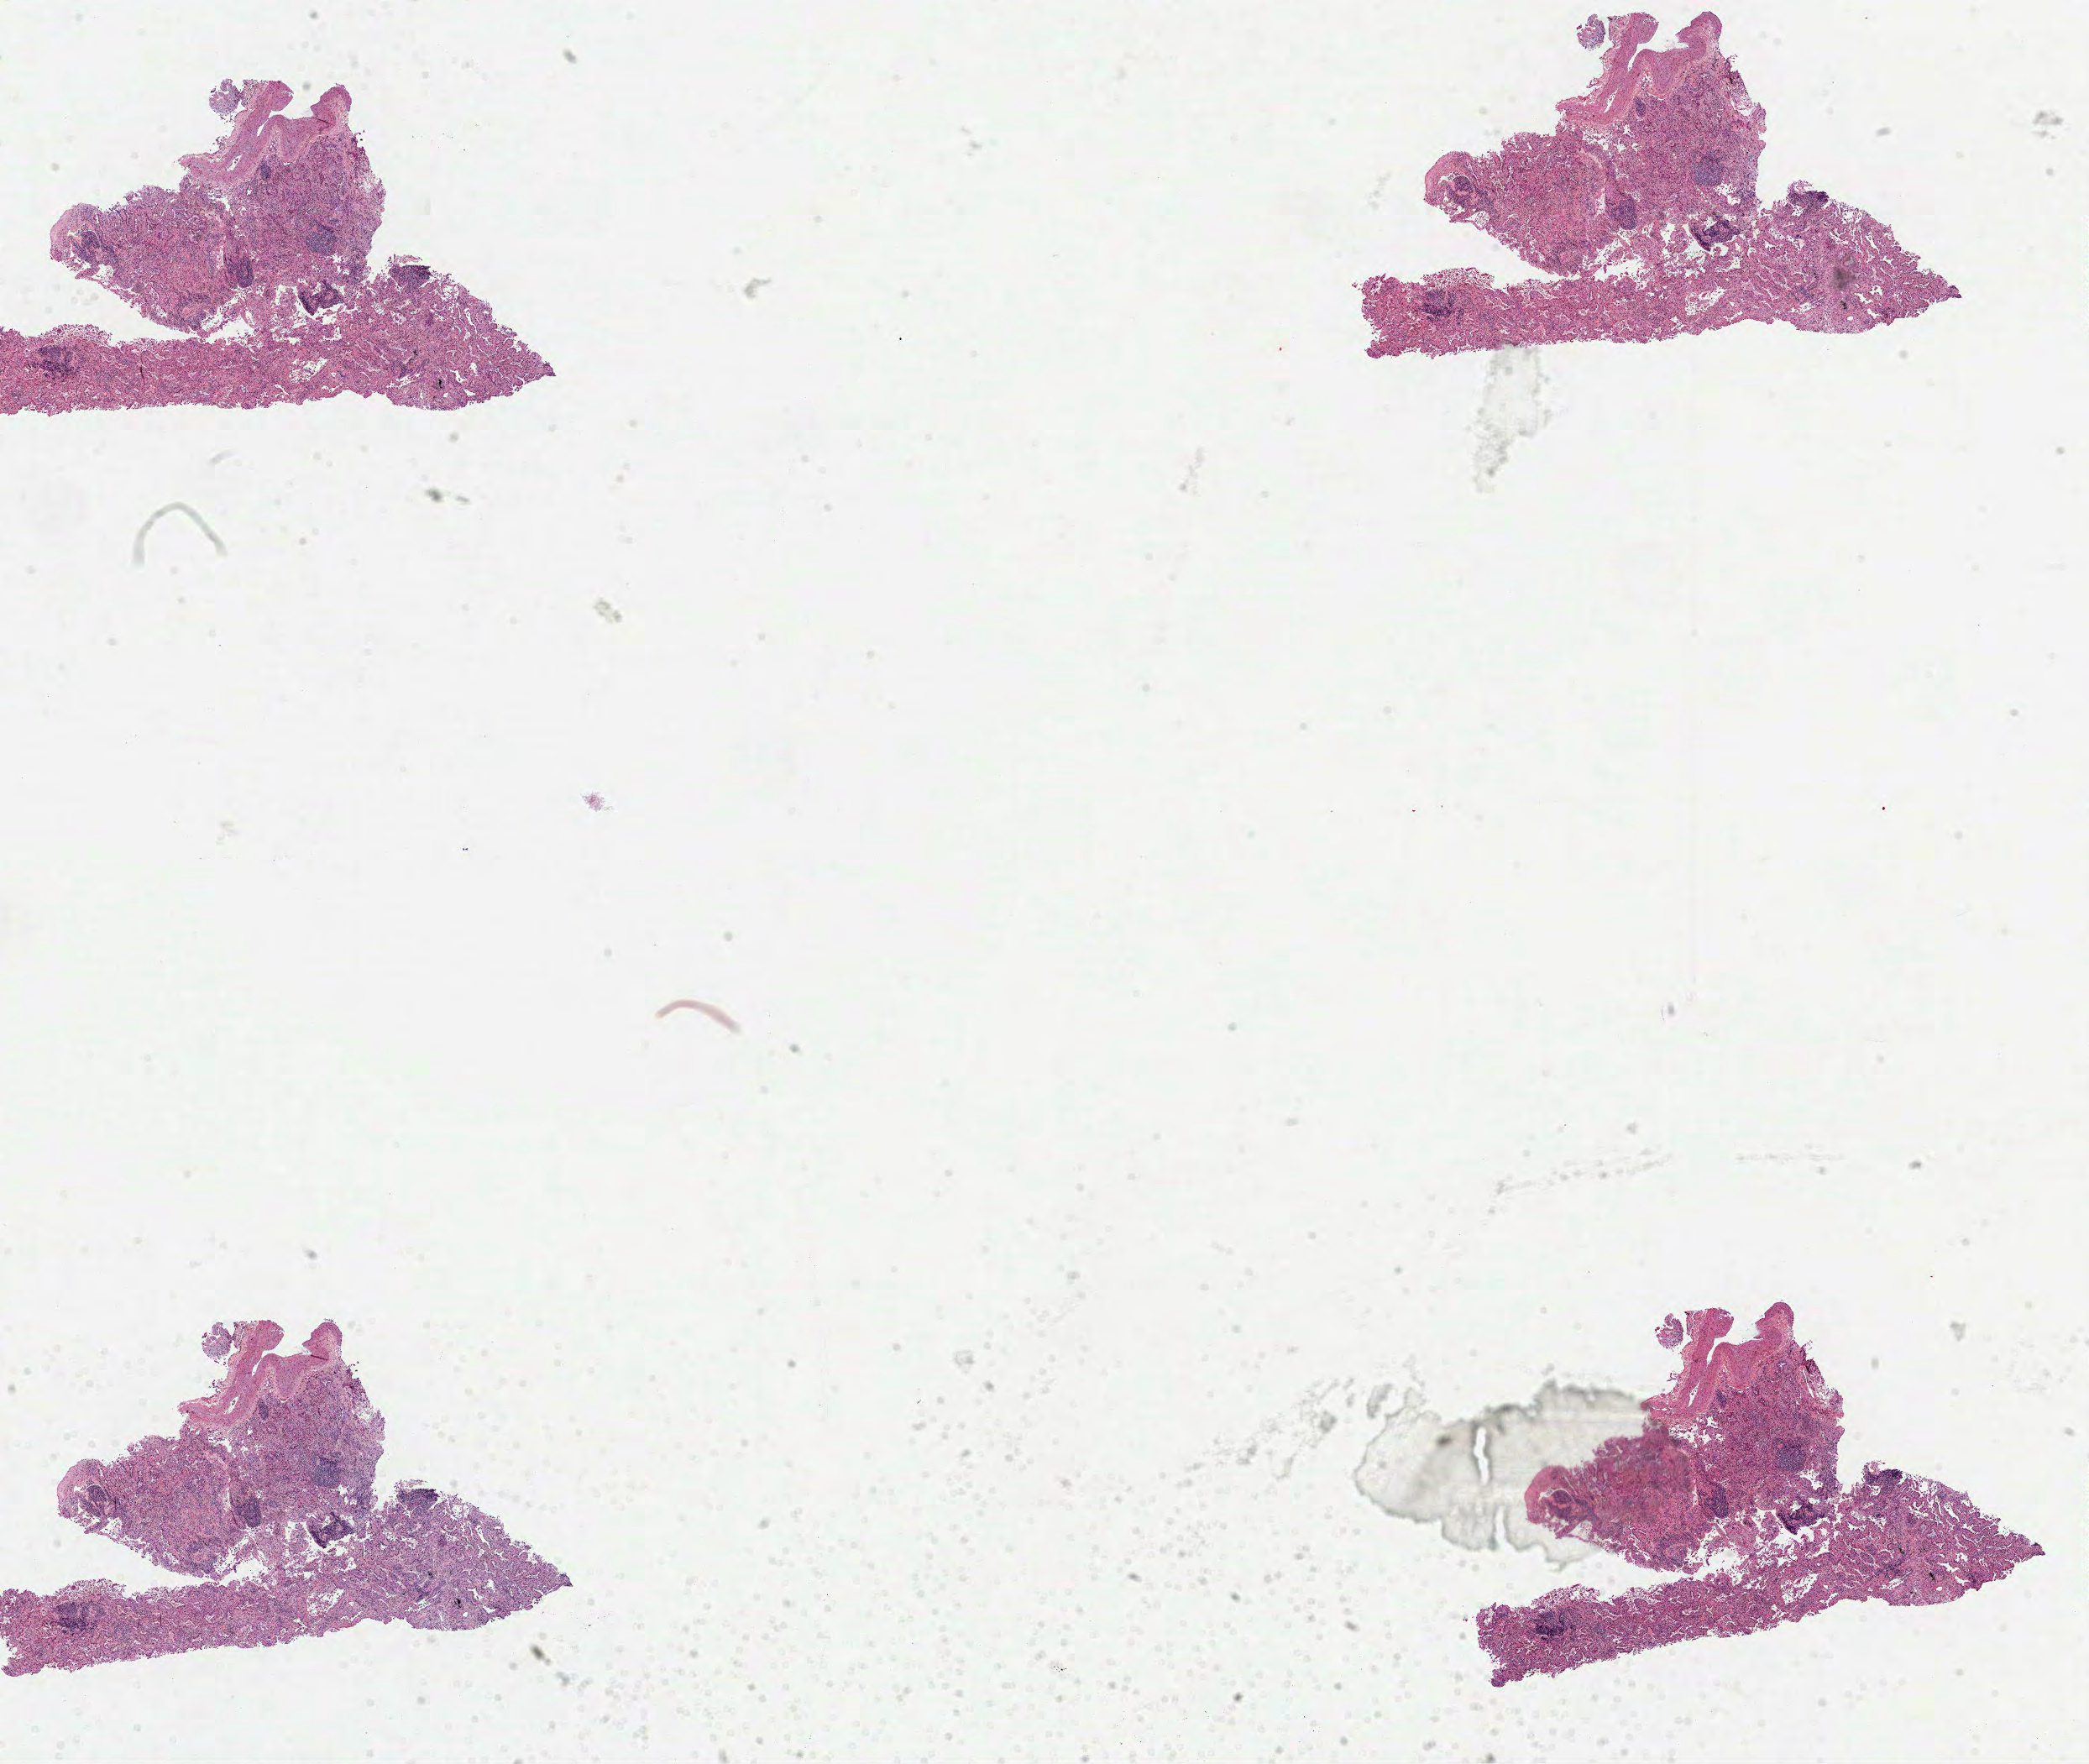
Hematoxylin and eosin (H&E) stained whole-slide image, a low-resolution overview of the entire scanned area, about 20.1 x 16.9 mm, formalin-fixed paraffin-embedded (FFPE) diagnostic section, lung, primary tumour sample. Female, age 74 years at initial diagnosis.
AJCC pathologic stage: IB (6th edition). Pathologic diagnosis: Adenocarcinoma, NOS (upper lobe, lung).